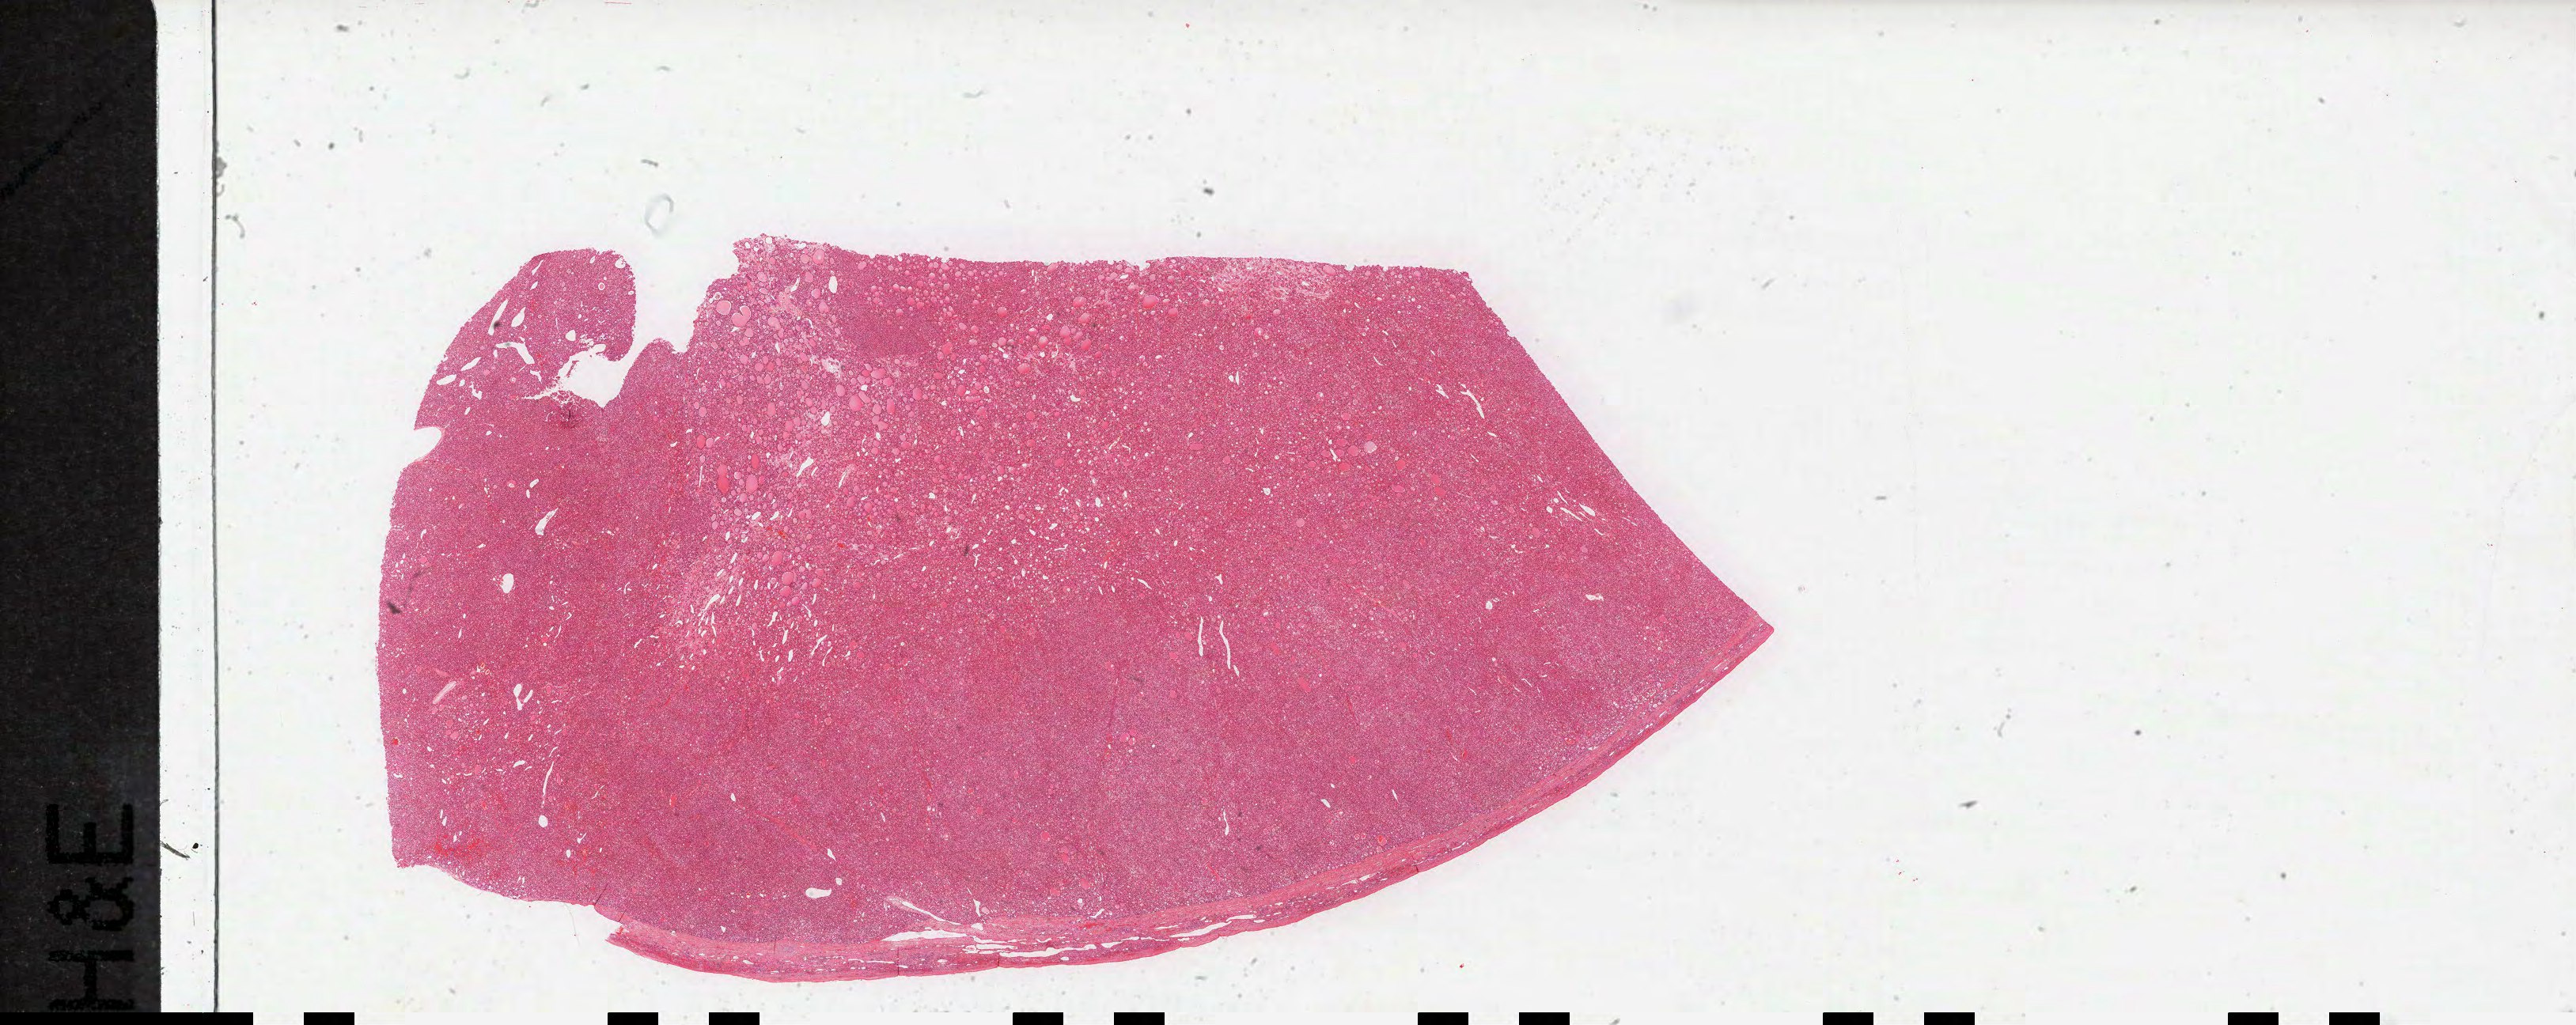
Whole-slide histology image, Hematoxylin and eosin (H&E) stained — low-resolution overview of the scanned area, about 52.7 x 21.0 mm. Formalin-fixed paraffin-embedded (FFPE) diagnostic section. Primary tumour sample from the liver. Female, age 79 years at initial diagnosis. Histologic grade: G1 (well differentiated).
* pathologic diagnosis: Hepatocellular carcinoma, NOS
* AJCC pathologic stage: II